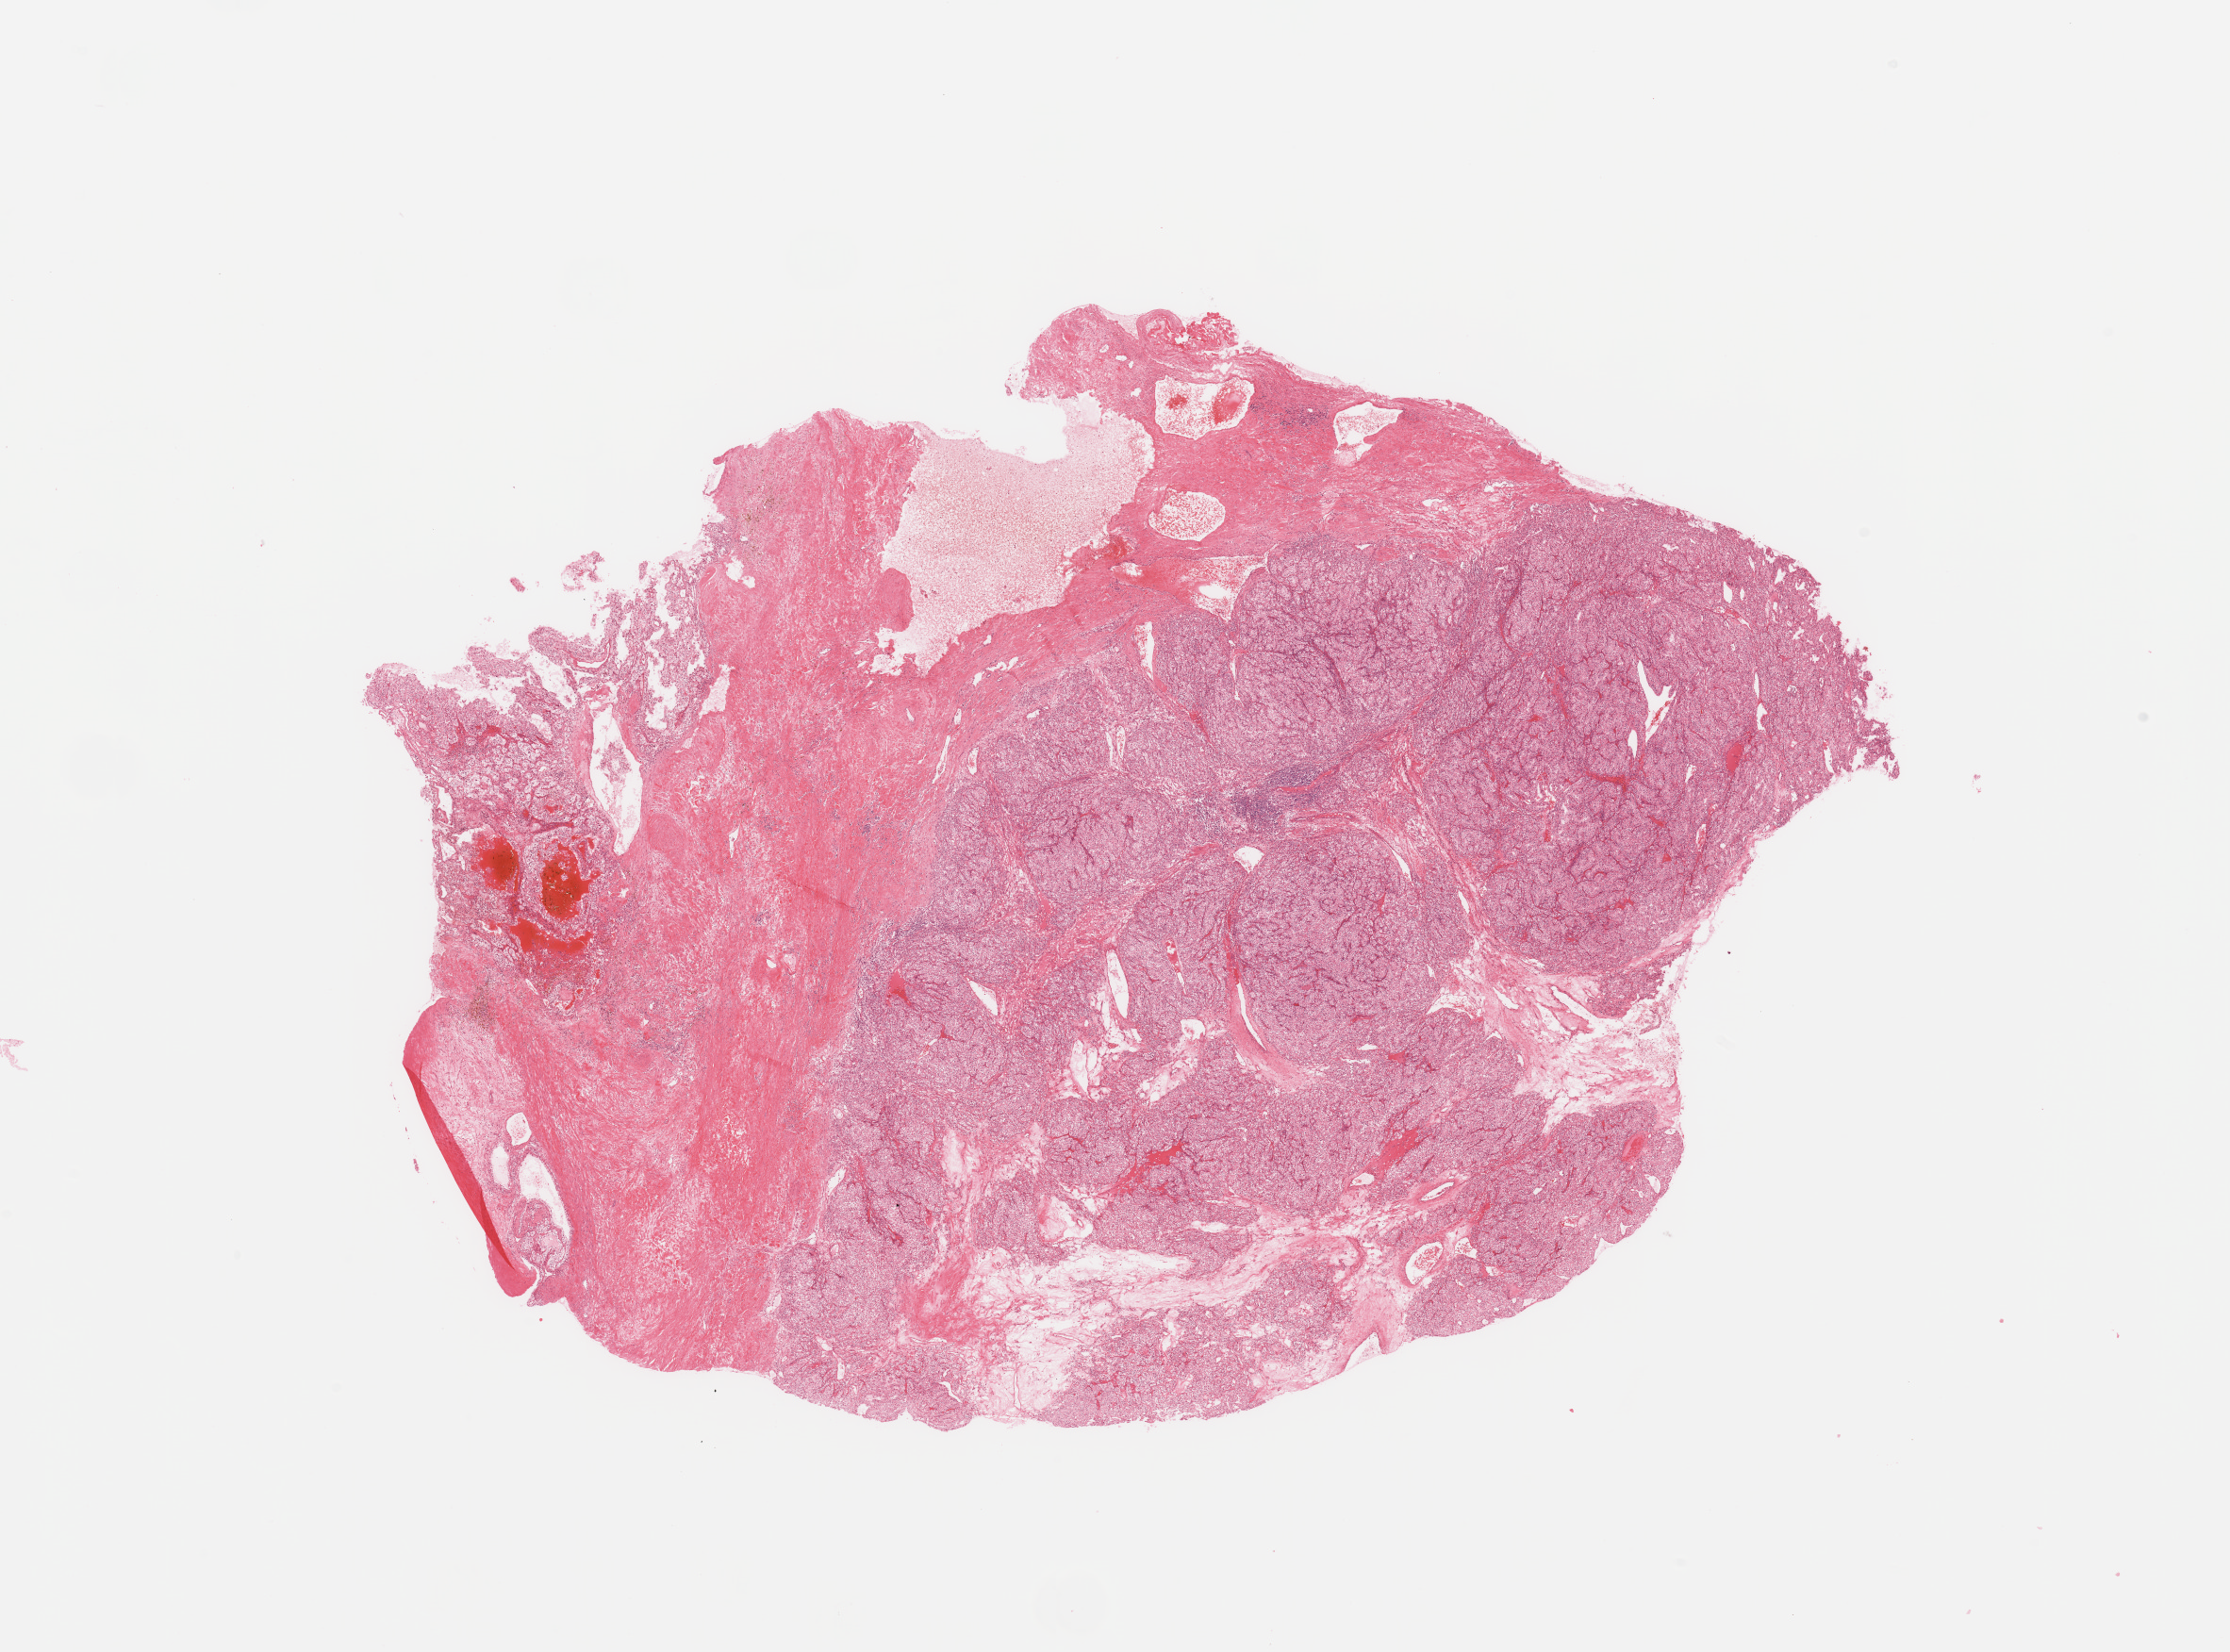
Hematoxylin and eosin (H&E) stained whole-slide image, shown as a low-resolution overview of the whole scanned area (about 18.7 x 13.9 mm, from a 20x scan). Tumour tissue sample, sampled site: kidney. 61-year-old male patient.
Diagnosis: Renal cell carcinoma, NOS.